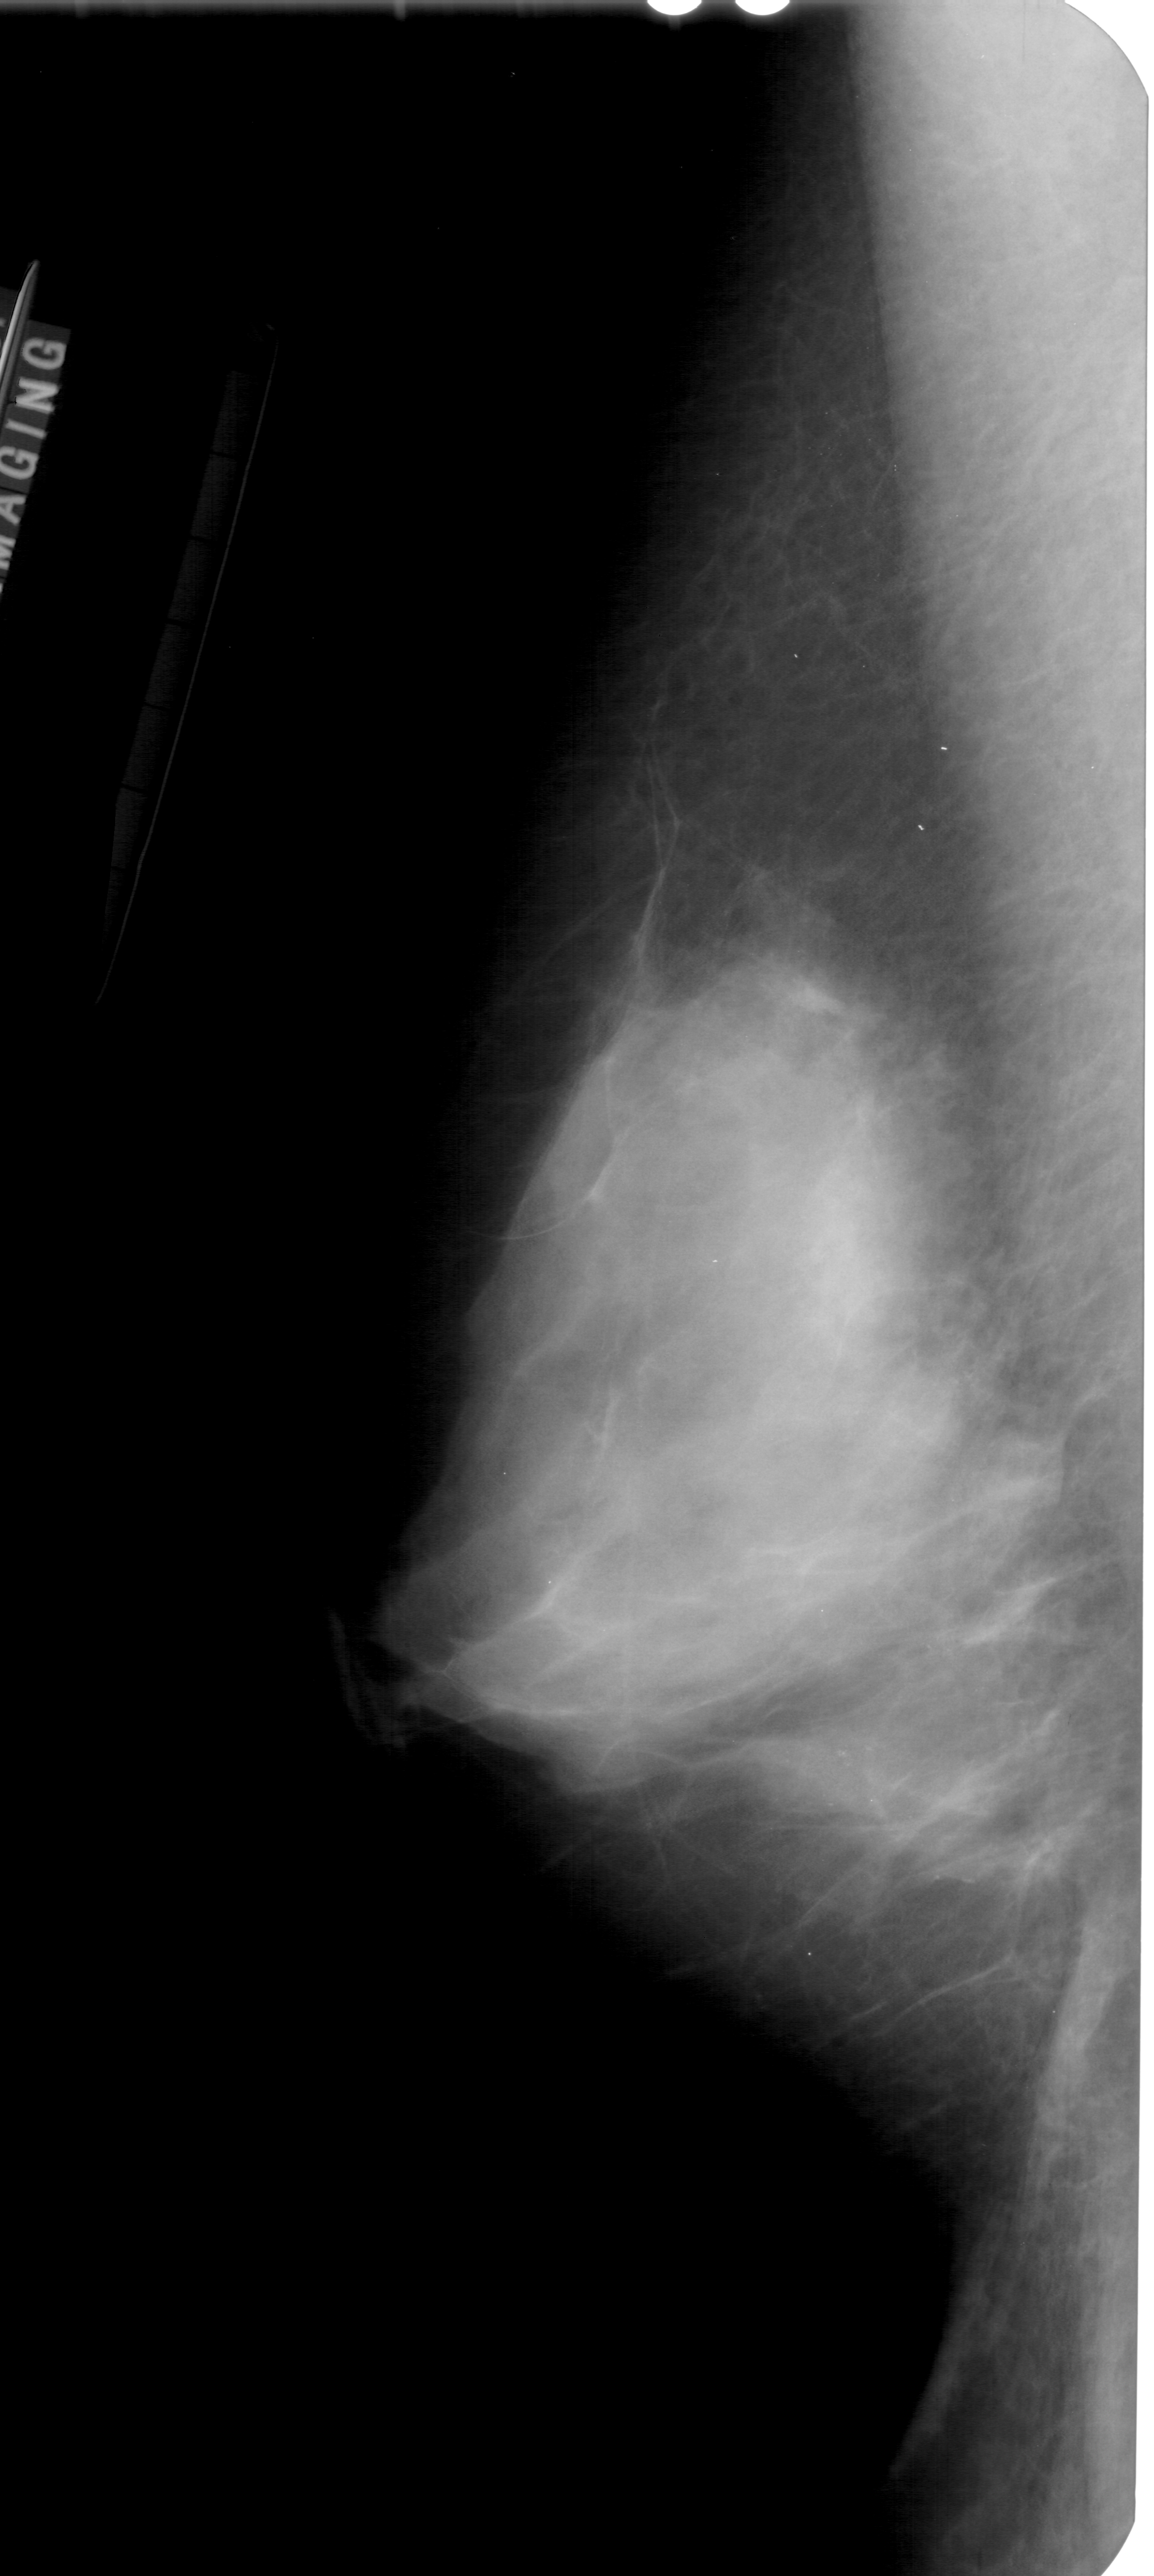
Mammogram (digitized film); left breast; mediolateral oblique (MLO) view; breast composition: extremely dense (BI-RADS density category 4 of 4); 1154 × 2576 image matrix.
Marked abnormalities (boxes around the expert regions of interest):
- calcifications, morphology pleomorphic, distribution clustered; BI-RADS assessment category 4; subtlety rating 2 on a 1 (subtle) to 5 (obvious) scale; pathology (as recorded): benign: bounding box [x1, y1, x2, y2] px = [762, 1723, 999, 1899]